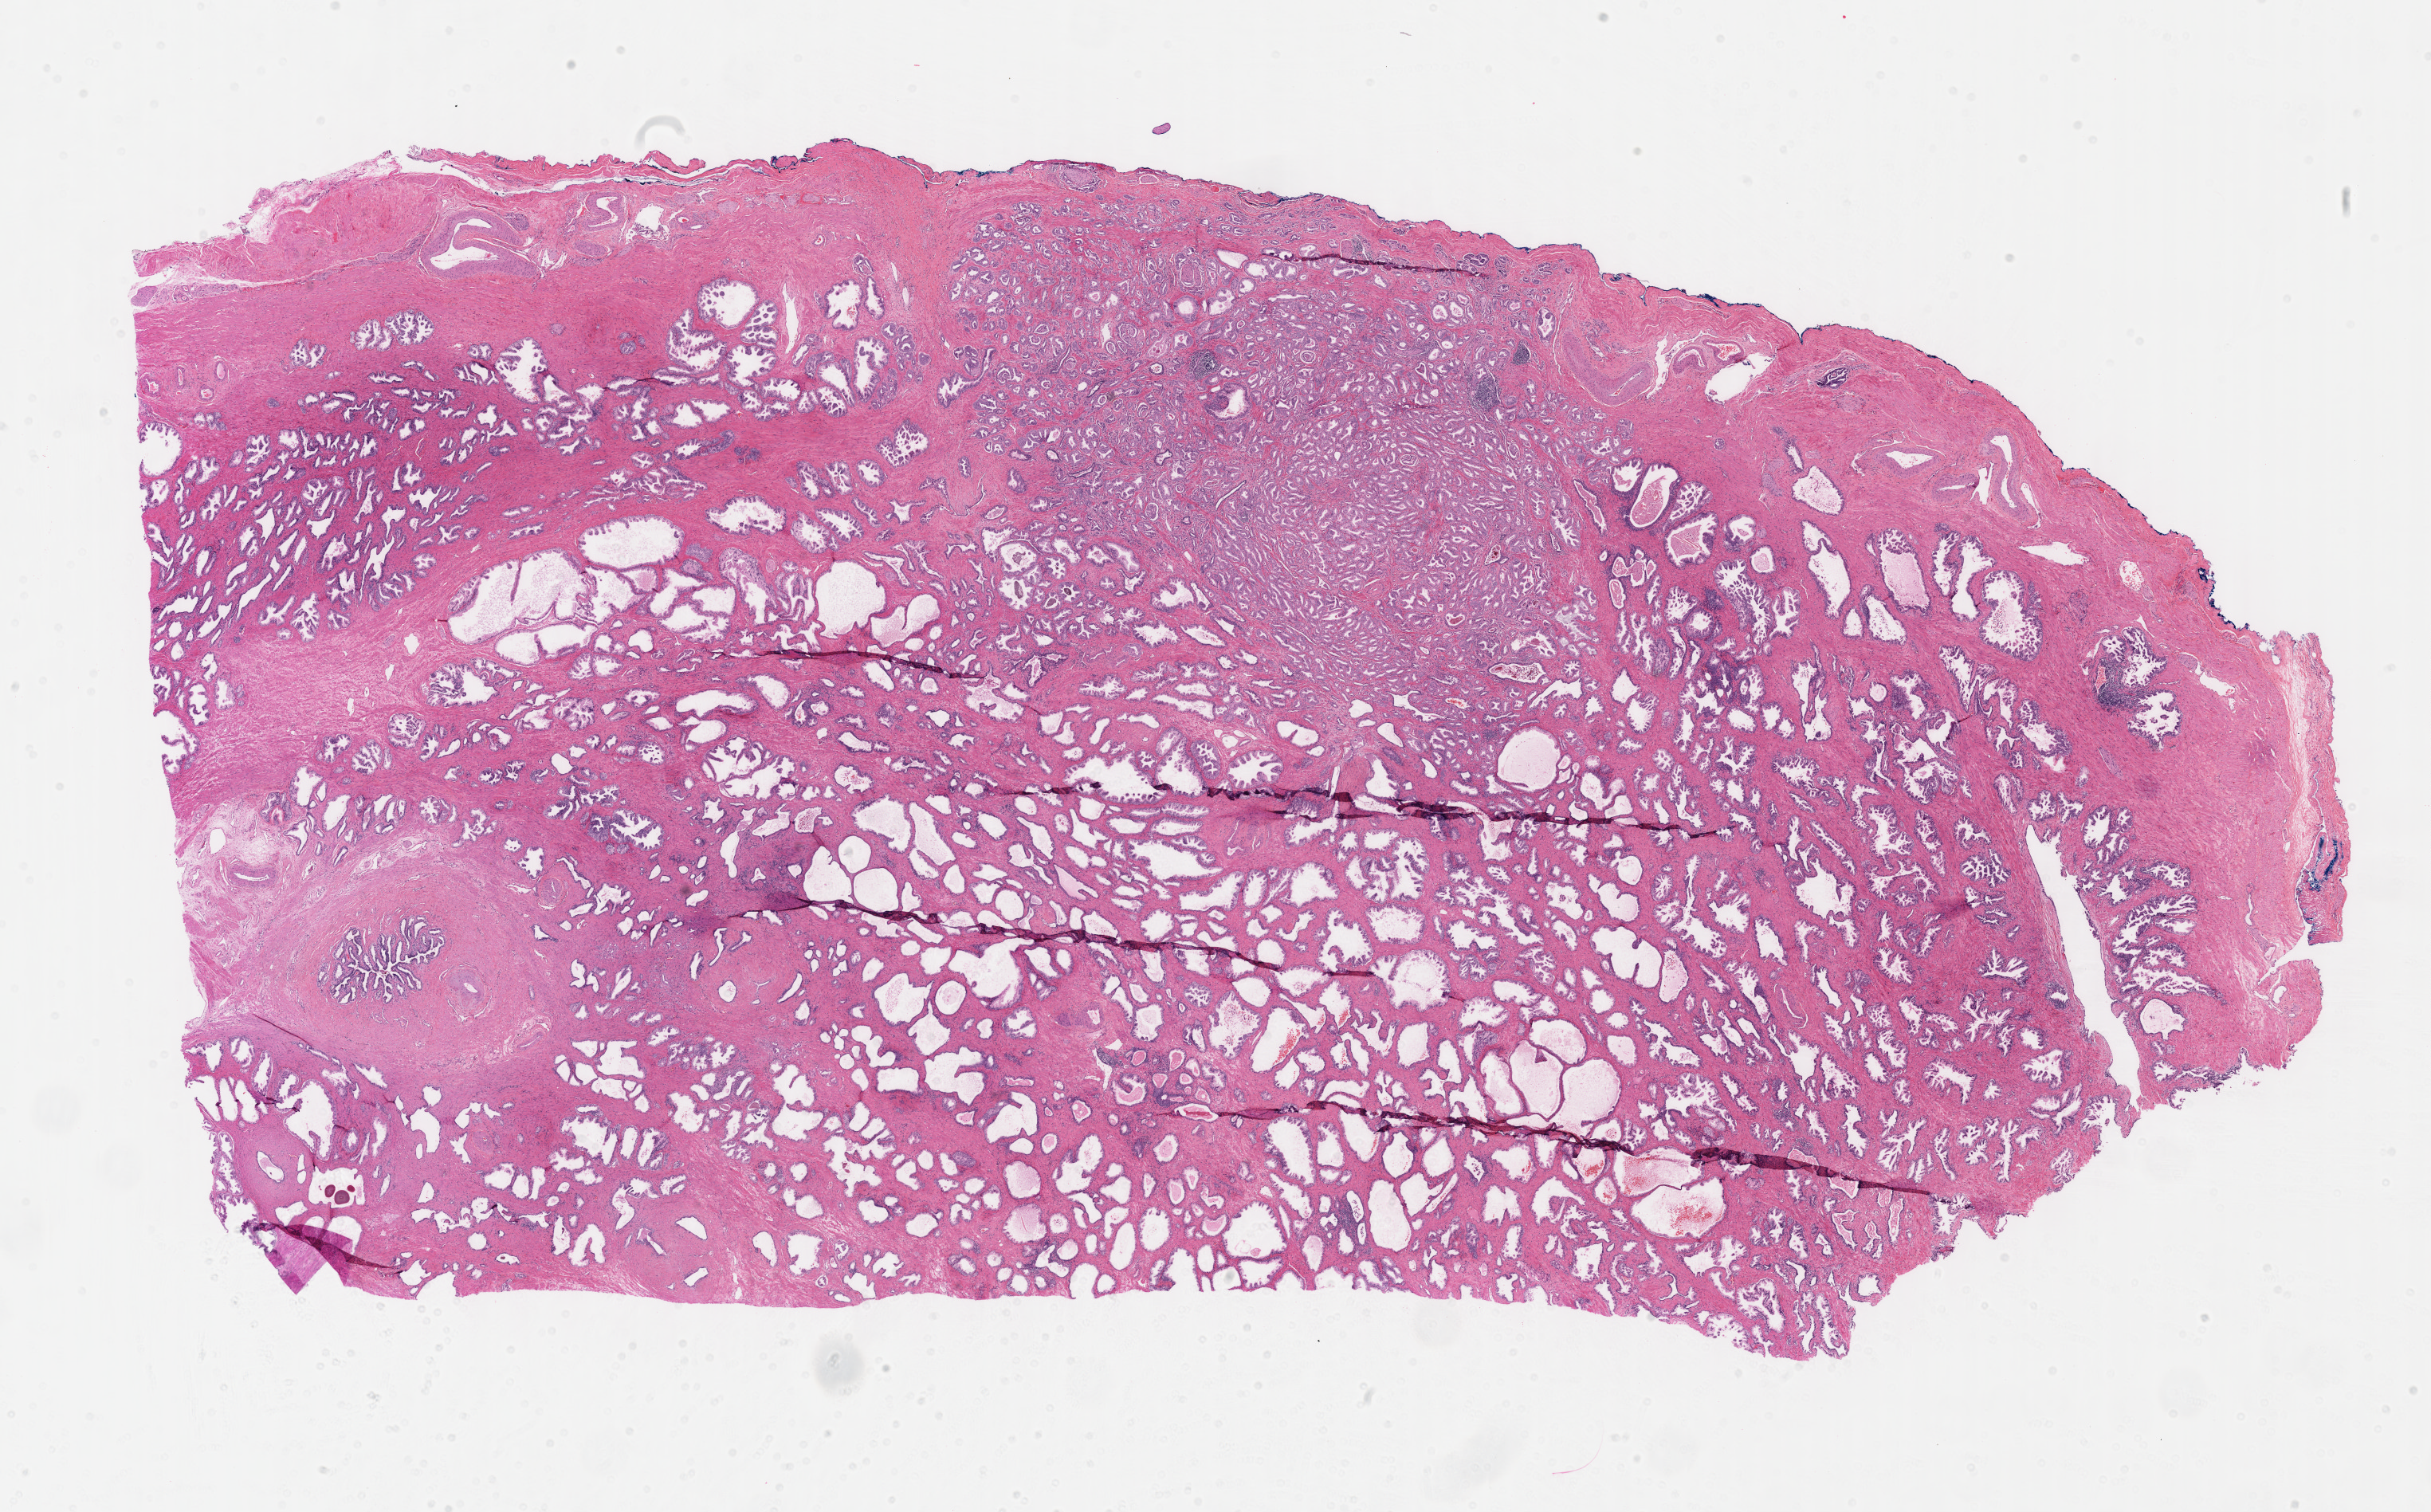
H&E whole-slide image — a low-resolution overview of the entire scanned area, about 24.6 x 15.3 mm (acquisition: 40x scan); formalin-fixed paraffin-embedded (FFPE) diagnostic section; prostate, primary tumour sample. Male patient; age at initial diagnosis 53 years. Gleason score: 6 (3+3).
Diagnosis: Adenocarcinoma, NOS (prostate gland). Lymph nodes positive (case pathology): 0 of 2 examined.